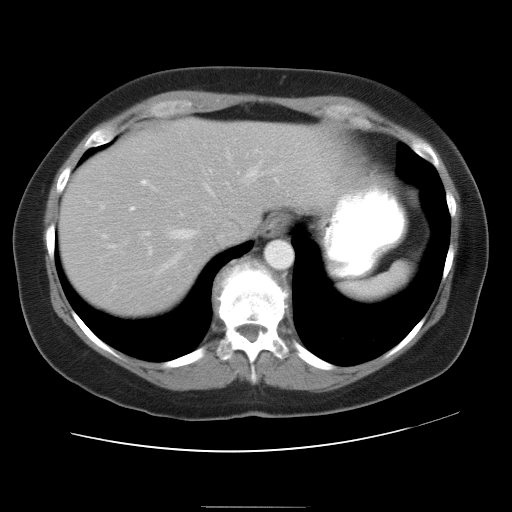
Contrast-enhanced abdominal CT, one axial slice; position 26 of 30 along the scan axis; reconstruction kernel STANDARD; intravenous contrast given; soft-tissue window (W 400 / L 40 HU); 7.5 mm slice thickness; 512 × 512 image matrix, field of view 376 × 376 mm. Female patient, age 52 years. Case-level facts recorded for this patient, not image findings: diagnosis: colorectal cancer liver metastases, imaged before liver resection; multiple liver metastases: no; largest metastasis: 3 cm; disease in both lobes: yes.
Structures marked on this image (expert manual segmentation):
- hepatic veins: bounding box (x1, y1, x2, y2) in pixels: (168, 169, 257, 265)
- liver: (58, 120, 333, 318)
- planned liver remnant (the part of the liver to remain after resection): (163, 120, 333, 227)
- portal vein (with intrahepatic branches): (130, 181, 146, 211)